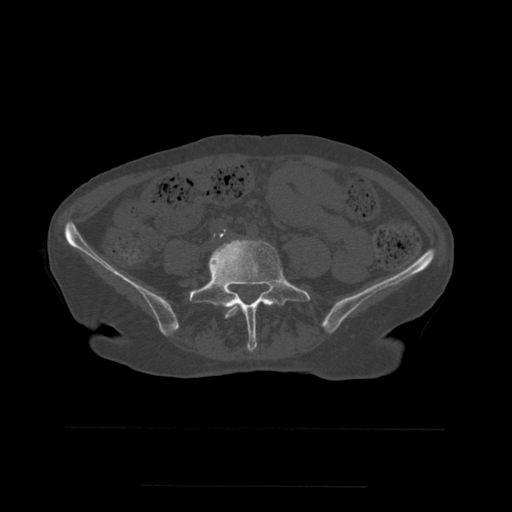
CT including the spine, one axial slice. Bone window (W 1800 / L 400 HU). 1.25 mm slice thickness. 512 × 512 image matrix. Patient age 58 years. From the clinical record (not read from this slice): primary cancer: lung.
Outlined on this slice (semi-automatic segmentation, software-assisted and operator-edited):
- L4 vertebra: bounding box (x1, y1, x2, y2) in pixels: (225, 304, 240, 319)
- L5 vertebra: (189, 240, 302, 352)